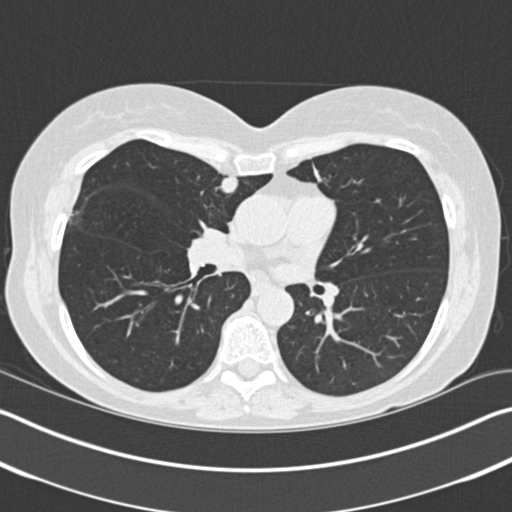
Low-dose screening chest CT, one axial slice; slice 98 of 183 in the series (ordered by position); reconstruction kernel B30f; 120 kVp; lung window (W 1500 / L -600 HU); 2 mm slice thickness; 512 × 512 image matrix, field of view 340 × 340 mm.
Annotated regions visible in this slice (expert manual segmentation):
- lesion 1 (tumor, upper lobe of right lung): bounding box (x1, y1, x2, y2) in pixels: (220, 176, 238, 193)